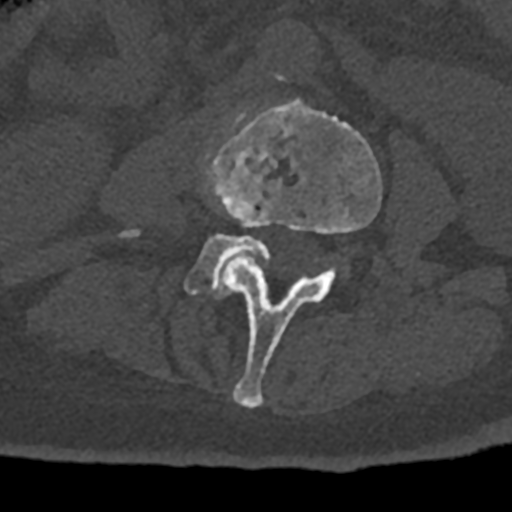
CT including the spine, one axial slice. Position 300 of 797 along the scan axis. Reconstruction kernel Br40s/3. 120 kVp. Bone window (W 1800 / L 400 HU). 512 × 512 image matrix, field of view 160 × 160 mm. Patient: male, 74 years. Case-level facts recorded for this patient, not image findings: primary cancer: renal; vertebrae with lytic lesions (as recorded): T10, L1, L2, L3, L4, L5.
Outlined on this slice (semi-automatic segmentation, software-assisted and operator-edited):
- L3 vertebra: box from (x=206, y=100) to (x=382, y=408) px
- L4 vertebra: (x=123, y=231)–(x=338, y=298)